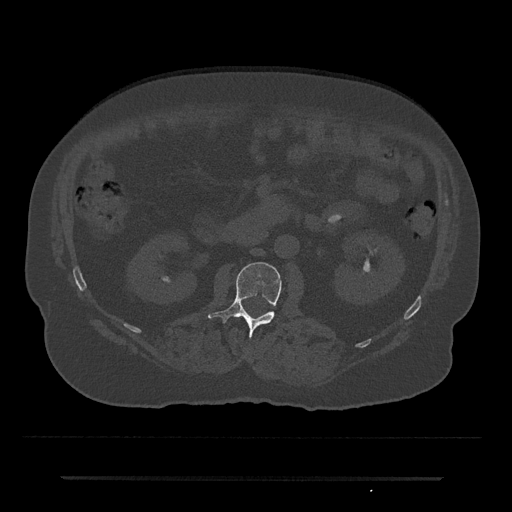
CT including the spine, one axial slice; slice 12 of 797 in the series (ordered by position); reconstruction kernel Br40s/3; bone window (W 1800 / L 400 HU); 0.5 mm slice thickness; 512 × 512 image matrix, field of view 437 × 437 mm. Male patient, age 69 years. Case-level facts recorded for this patient, not image findings: primary cancer: prostate.
Annotated regions visible in this slice (semi-automatic segmentation, software-assisted and operator-edited):
- L2 vertebra: bounding box [x1, y1, x2, y2] px = [208, 262, 282, 338]